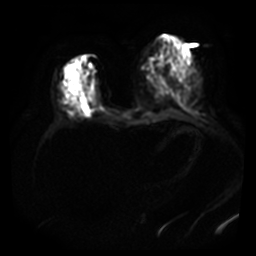
Breast MRI, one axial slice. Position 17 of 40 along the scan axis. Diffusion-weighted series; image 2 of 4 stored at this slice position (different b-values; order by instance number). 3 T. 256 × 256 image matrix. Female patient.
Outlined on this slice (expert manual segmentation):
- tumour on diffusion-weighted imaging: box from (x=64, y=96) to (x=81, y=107) px